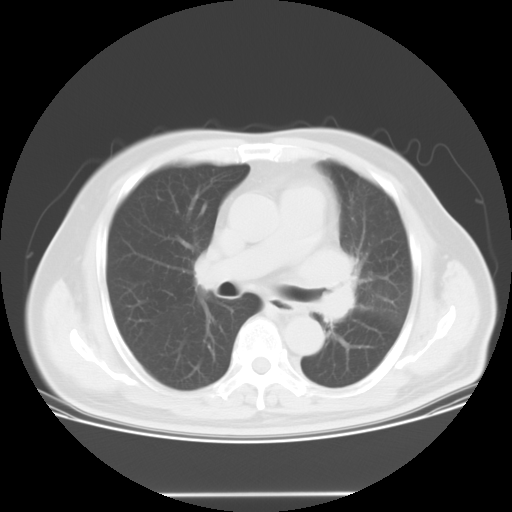
Chest CT, one axial slice; position 17 of 28 along the scan axis; 120 kVp; lung window (W 1500 / L -600 HU); 10 mm slice thickness; 512 × 512 image matrix, field of view 398 × 398 mm. Male patient, age 61 years. From the clinical record (not read from this slice): clinical TNM (as recorded): T3 N1 M1.
Annotated regions visible in this slice (rectangle marked by the reading radiologist):
- lung tumour (recorded histology: small cell carcinoma): bounding box <321,236,367,327> (left, top, right, bottom; pixels)